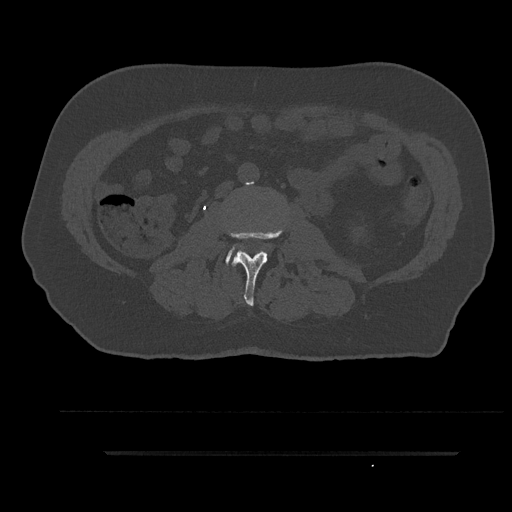
CT including the spine, one axial slice. Position 83 of 797 along the scan axis. Reconstruction kernel Br40s/3. Bone window (W 1800 / L 400 HU). 0.5 mm slice thickness. 512 × 512 image matrix, field of view 432 × 432 mm. Patient: male, 63 years. Case-level facts recorded for this patient, not image findings: primary cancer: renal.
Outlined on this slice (semi-automatic segmentation, software-assisted and operator-edited):
- L2 vertebra: bounding box [x1, y1, x2, y2] px = [227, 228, 284, 306]
- L3 vertebra: [226, 249, 242, 265]